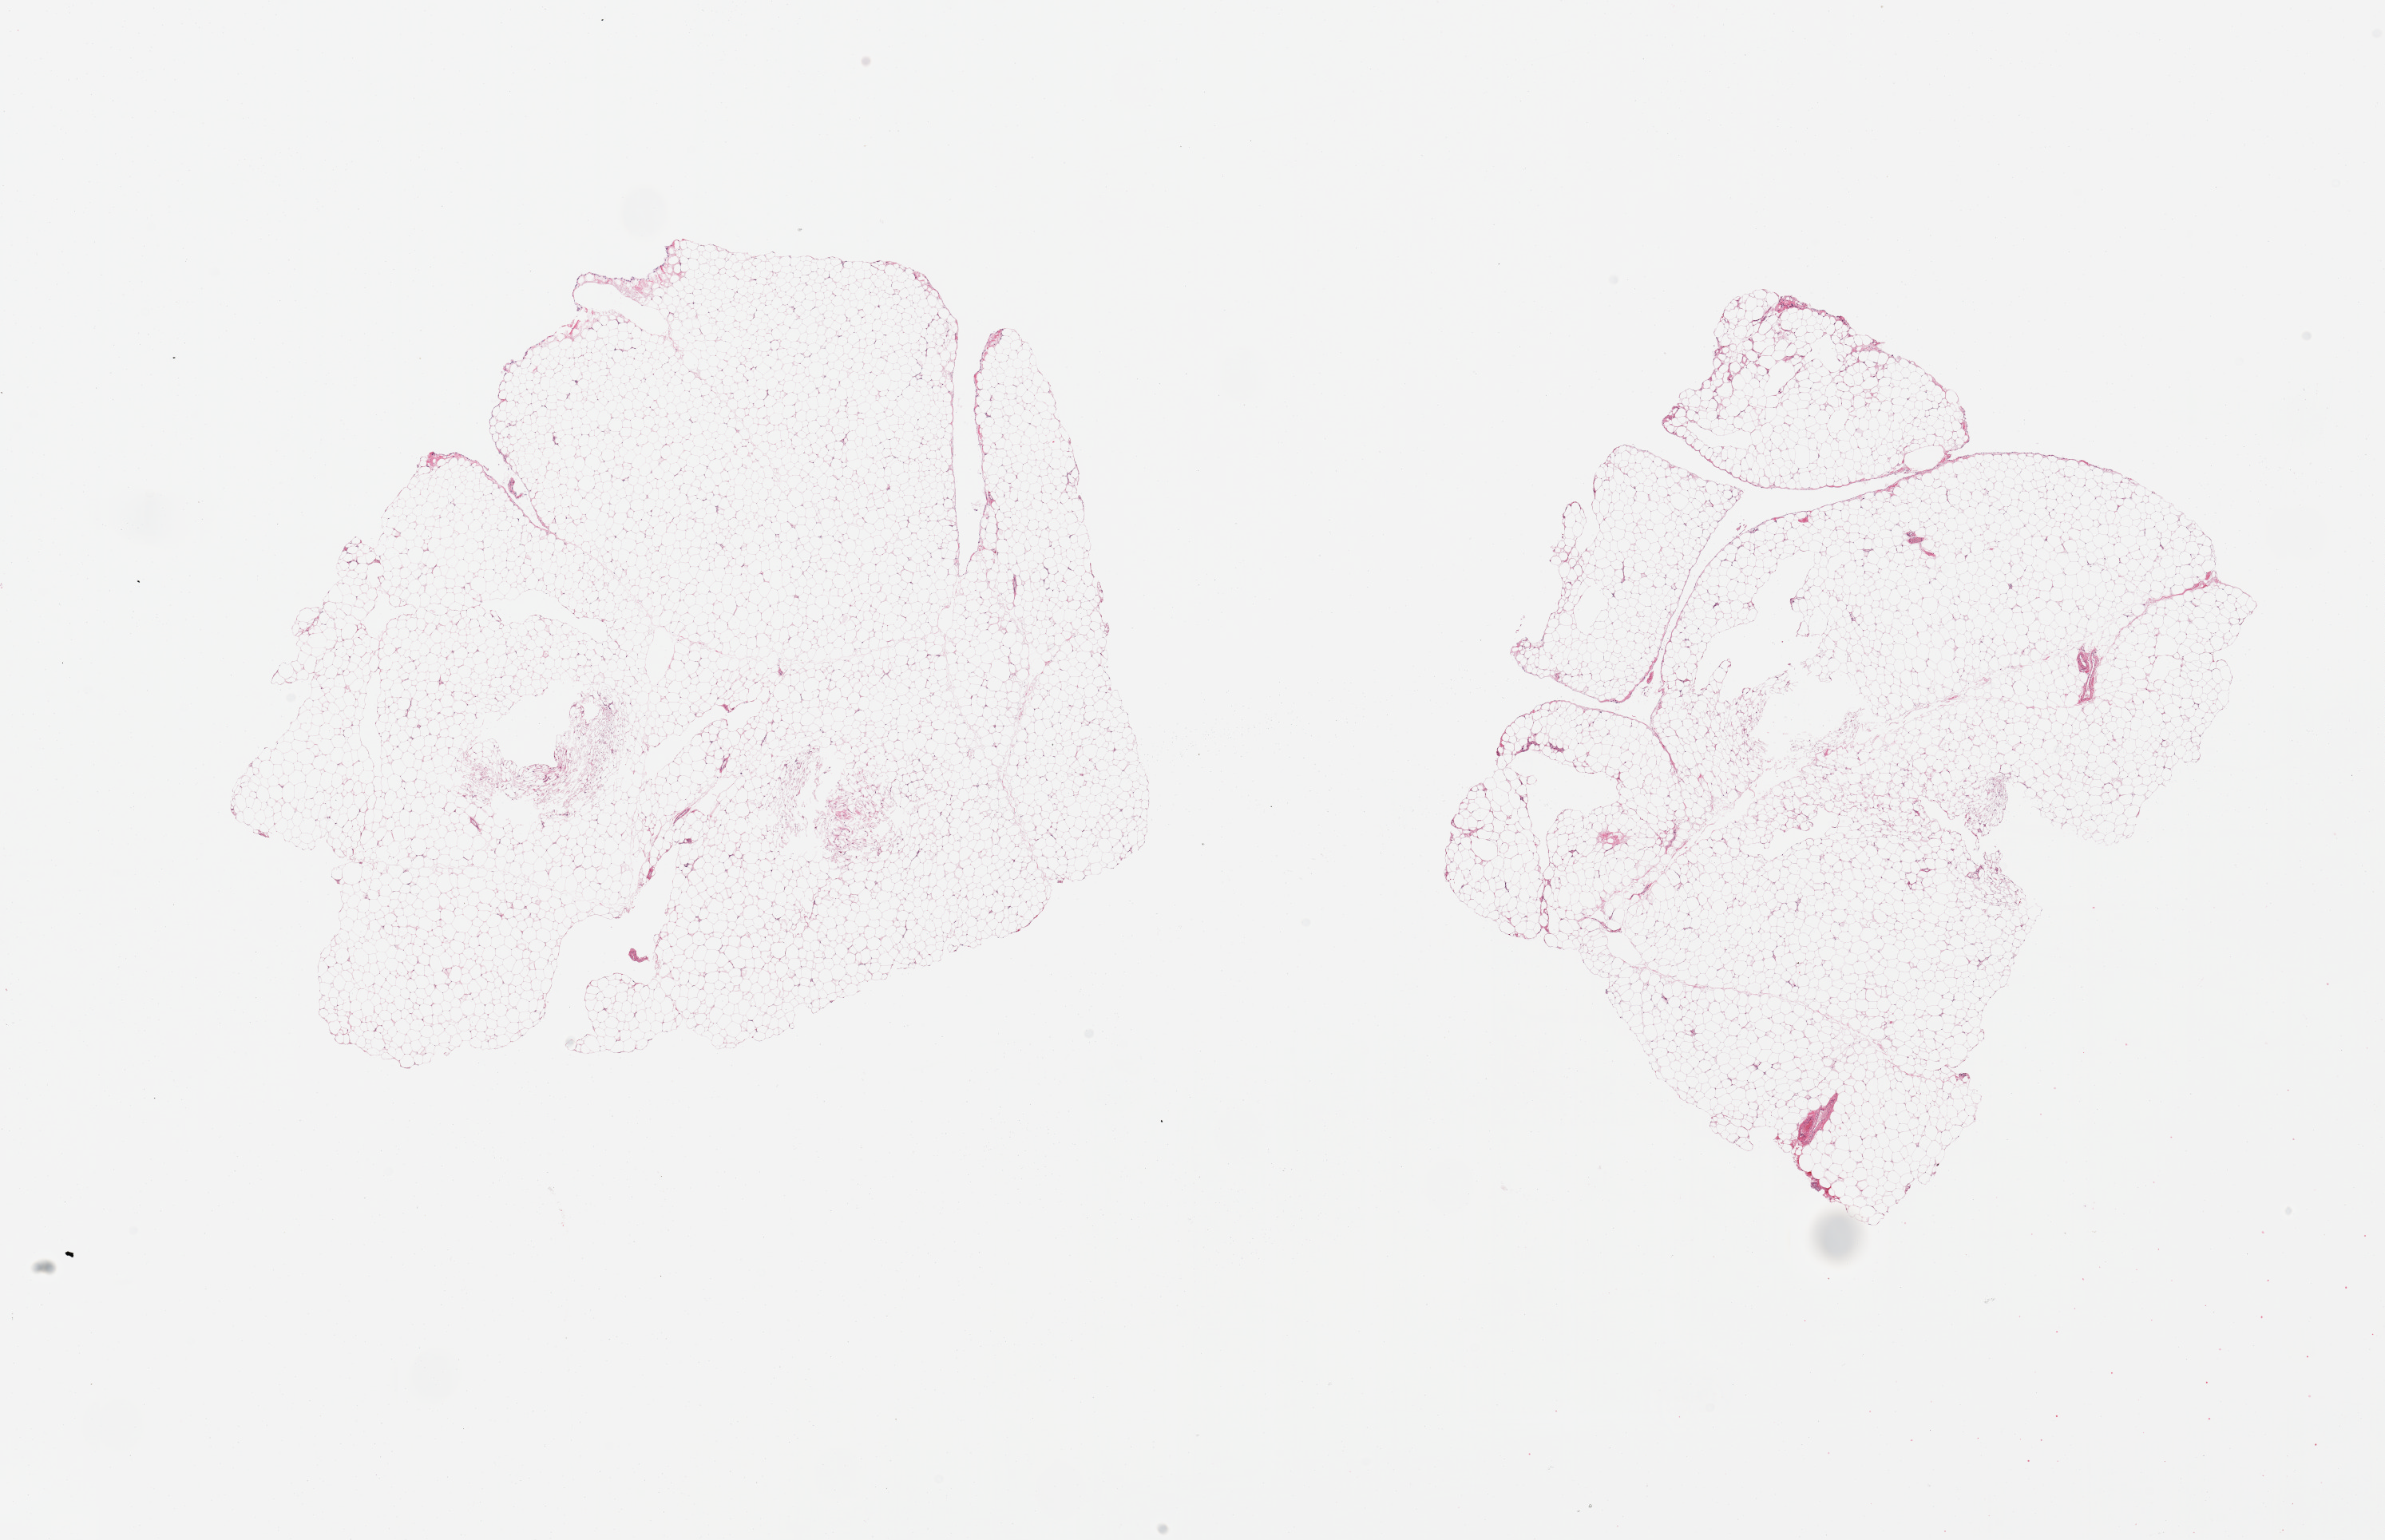
Digitized H&E-stained section, brightfield, whole scanned area (about 23.6 x 15.3 mm, acquisition: 20x scan) shown as a low-resolution overview. PAXgene-fixed, paraffin-embedded tissue. Sampled site (target tissue): omentum. Donor tissue sample. Male donor.
• reviewer comment on this tissue sample: 2 pieces, only trace fascia